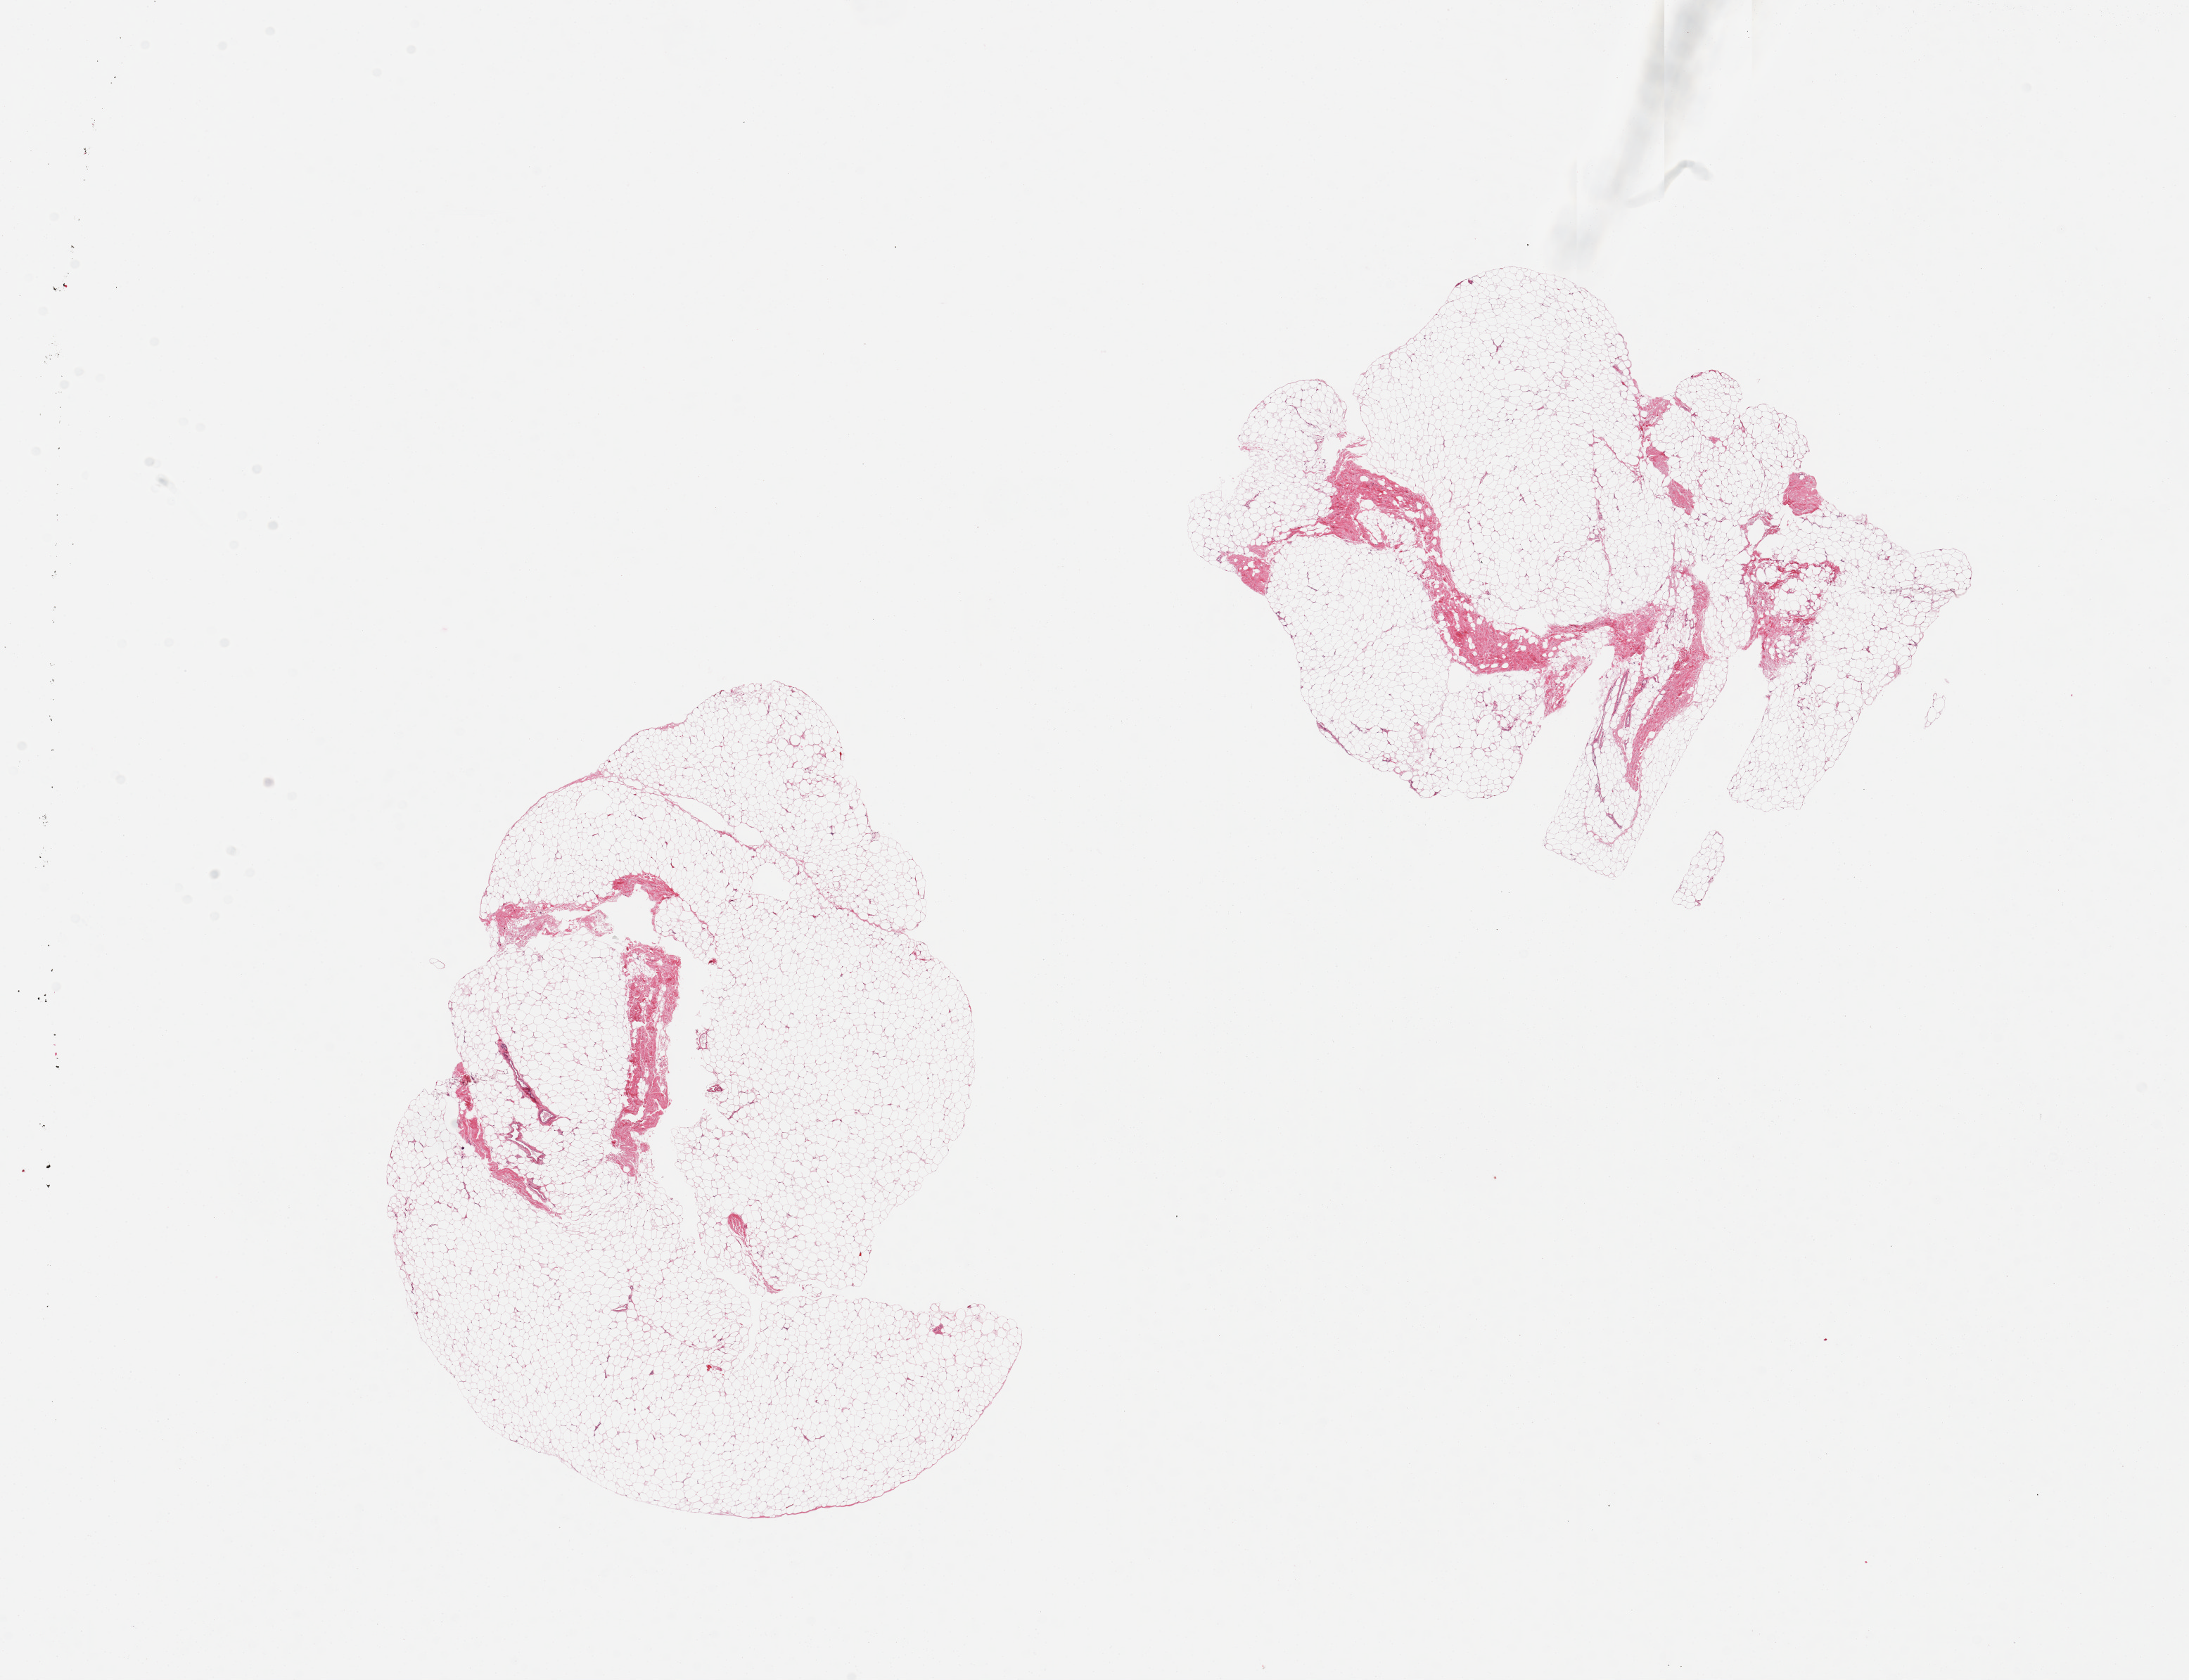
Digitized H&E-stained section, a low-resolution overview of the entire scanned area, about 24.6 x 18.9 mm; PAXgene-fixed paraffin-embedded (PFPE) section; sampled site (target tissue): breast; tissue donor sample.
- review note (as recorded): 2 pieces, fibroadipose tissue only, no ductal elements noted